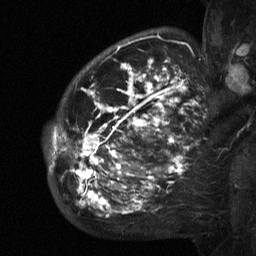
Breast MRI (dynamic contrast-enhanced), one sagittal slice. Position 45 of 64 along the scan axis. Dynamic contrast-enhanced study with each time point stored as its own series, time point 2 of 3 at this slice position (early post-contrast, ordered by acquisition time). 1.5 T. TE 4.8 ms, TR 27 ms. 2.3 mm slice thickness. 256 × 256 image matrix, field of view 200 × 200 mm. Female patient, age 50 years. From the clinical record (not read from this slice): setting: breast cancer imaged before/during neoadjuvant chemotherapy; receptor status: HER2-positive.
Outlined on this slice (semi-automatically segmented with operator editing):
- analysis volume of interest (the breast-tissue region the enhancement analysis was run in; not a lesion): bounding box <53,64,211,218> (left, top, right, bottom; pixels)
- tumour enhancement mask (voxels above the 90 % enhancement threshold inside the analysis volume of interest): <53,64,200,216>